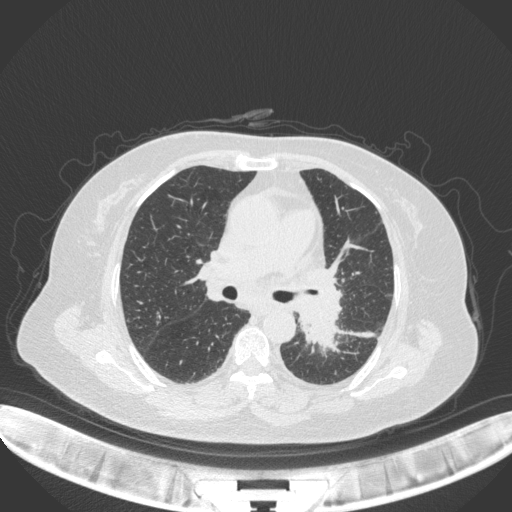
Chest CT, one axial slice; position 205 of 328 along the scan axis; lung window (W 1500 / L -600 HU); 1 mm slice thickness; 512 × 512 image matrix, field of view 400 × 400 mm. Female patient, age 69 years. From the clinical record (not read from this slice): clinical TNM (as recorded): T2b N3 M1.
Structures marked on this image (bounding box drawn by a radiologist):
- lung tumour (recorded histology: adenocarcinoma): bounding box (x1, y1, x2, y2) in pixels: (294, 302, 338, 355)